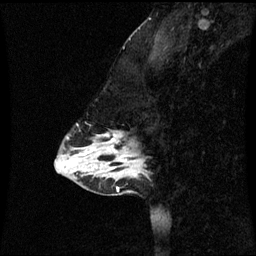
Breast MRI (dynamic contrast-enhanced), one sagittal slice. Slice 19 of 60 in the series (ordered by position). Dynamic contrast-enhanced series, image 2 of 3 at this slice position (ordered by acquisition). 1.5 T. TE 4.2 ms, TR 8.9 ms. 2 mm slice thickness. 256 × 256 image matrix, field of view 220 × 220 mm. Patient: female, 43 years. Case-level facts recorded for this patient, not image findings: setting: breast cancer imaged before/during neoadjuvant chemotherapy; receptor status: HR-positive, HER2-negative.
Outlined on this slice (semi-automatic segmentation, software-assisted and operator-edited):
- analysis volume of interest (the breast-tissue region the enhancement analysis was run in; not a lesion): bounding box (x1, y1, x2, y2) in pixels: (84, 134, 144, 171)
- tumour enhancement mask (voxels above the 70 % enhancement threshold inside the analysis volume of interest): (104, 134, 126, 161)